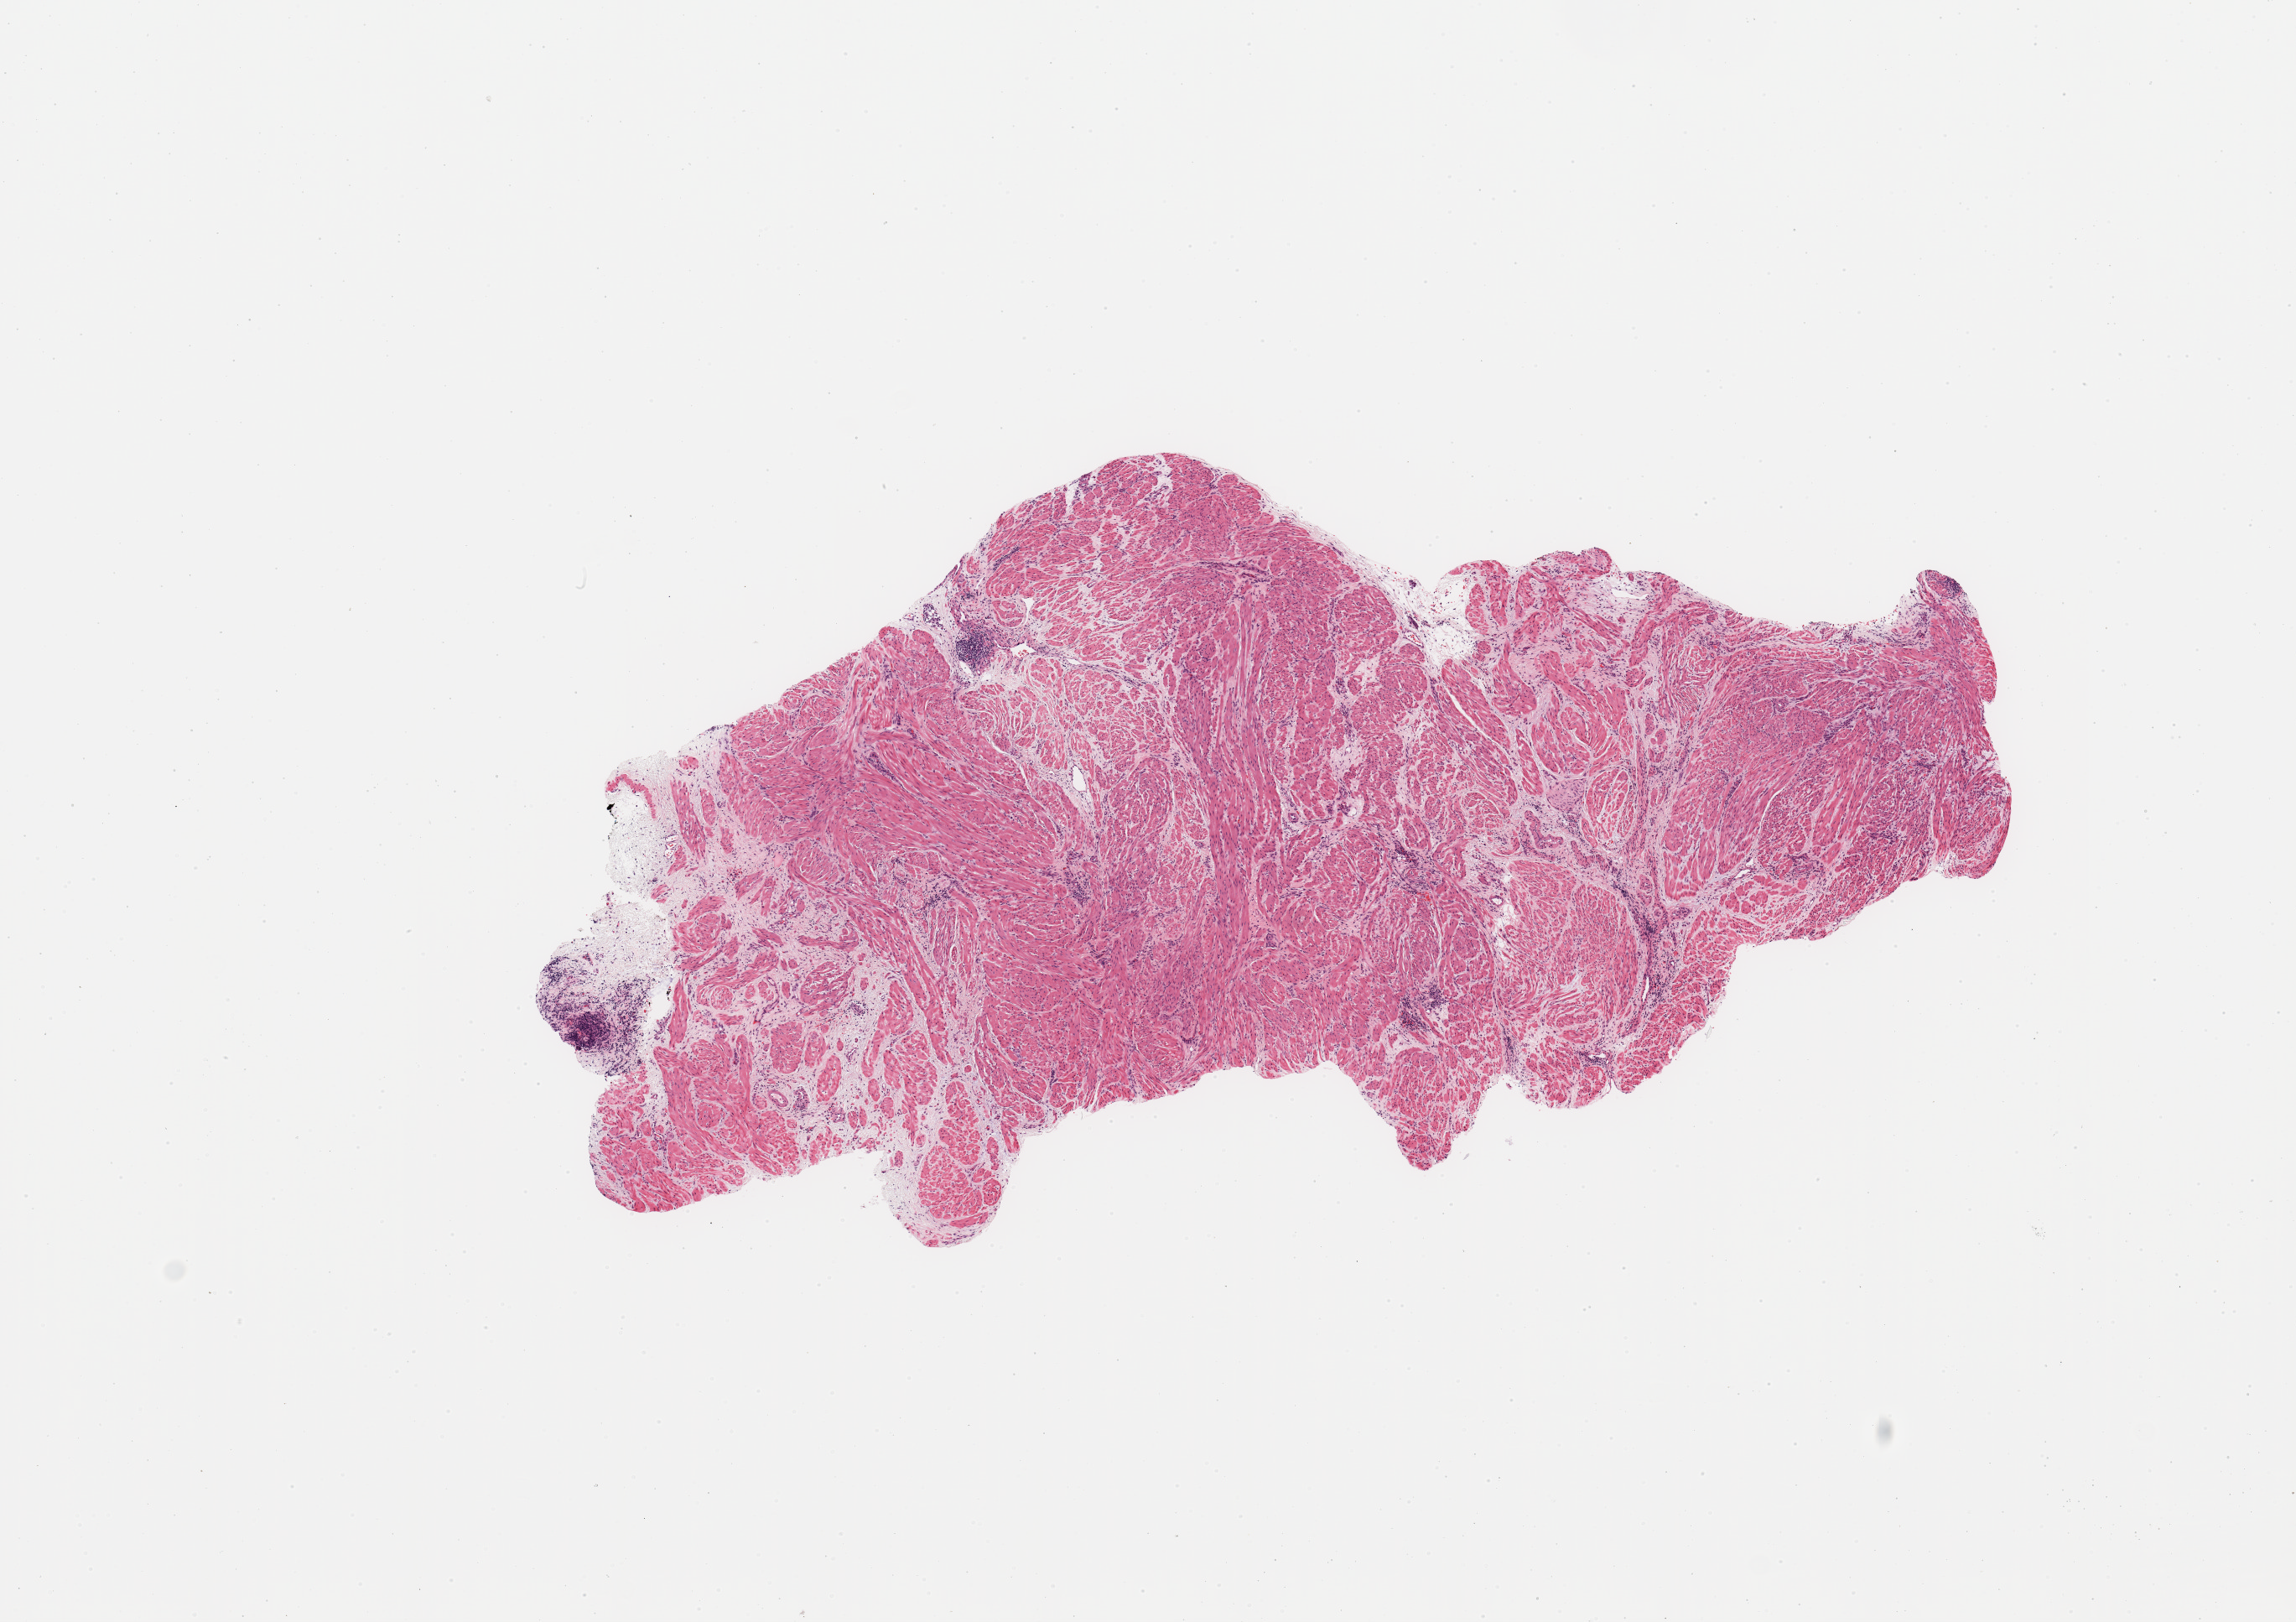
Whole-slide histology image, Hematoxylin and eosin (H&E) stained, shown as a low-resolution overview of the whole scanned area (about 10.8 x 7.6 mm), uterus, normal (non-tumour) tissue. Patient: female, age 59 years.
This section: normal (non-tumour) tissue from the same patient. Patient diagnosis: Endometrioid adenocarcinoma, NOS.